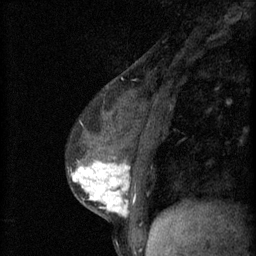
Breast MRI (dynamic contrast-enhanced), one sagittal slice; slice 22 of 60 in the series (ordered by position); 3 images stored at this slice position (order not interpretable as contrast timing); 1.5 T; TE 4.2 ms, TR 11 ms; 256 × 256 image matrix. Female patient, age 37 years.
Structures marked on this image (semi-automatically segmented with operator editing):
- analysis volume of interest (the breast-tissue region the enhancement analysis was run in; not a lesion): bounding box <68,138,174,221> (left, top, right, bottom; pixels)
- tumour enhancement mask (voxels above the 70 % enhancement threshold inside the analysis volume of interest): <72,162,130,217>